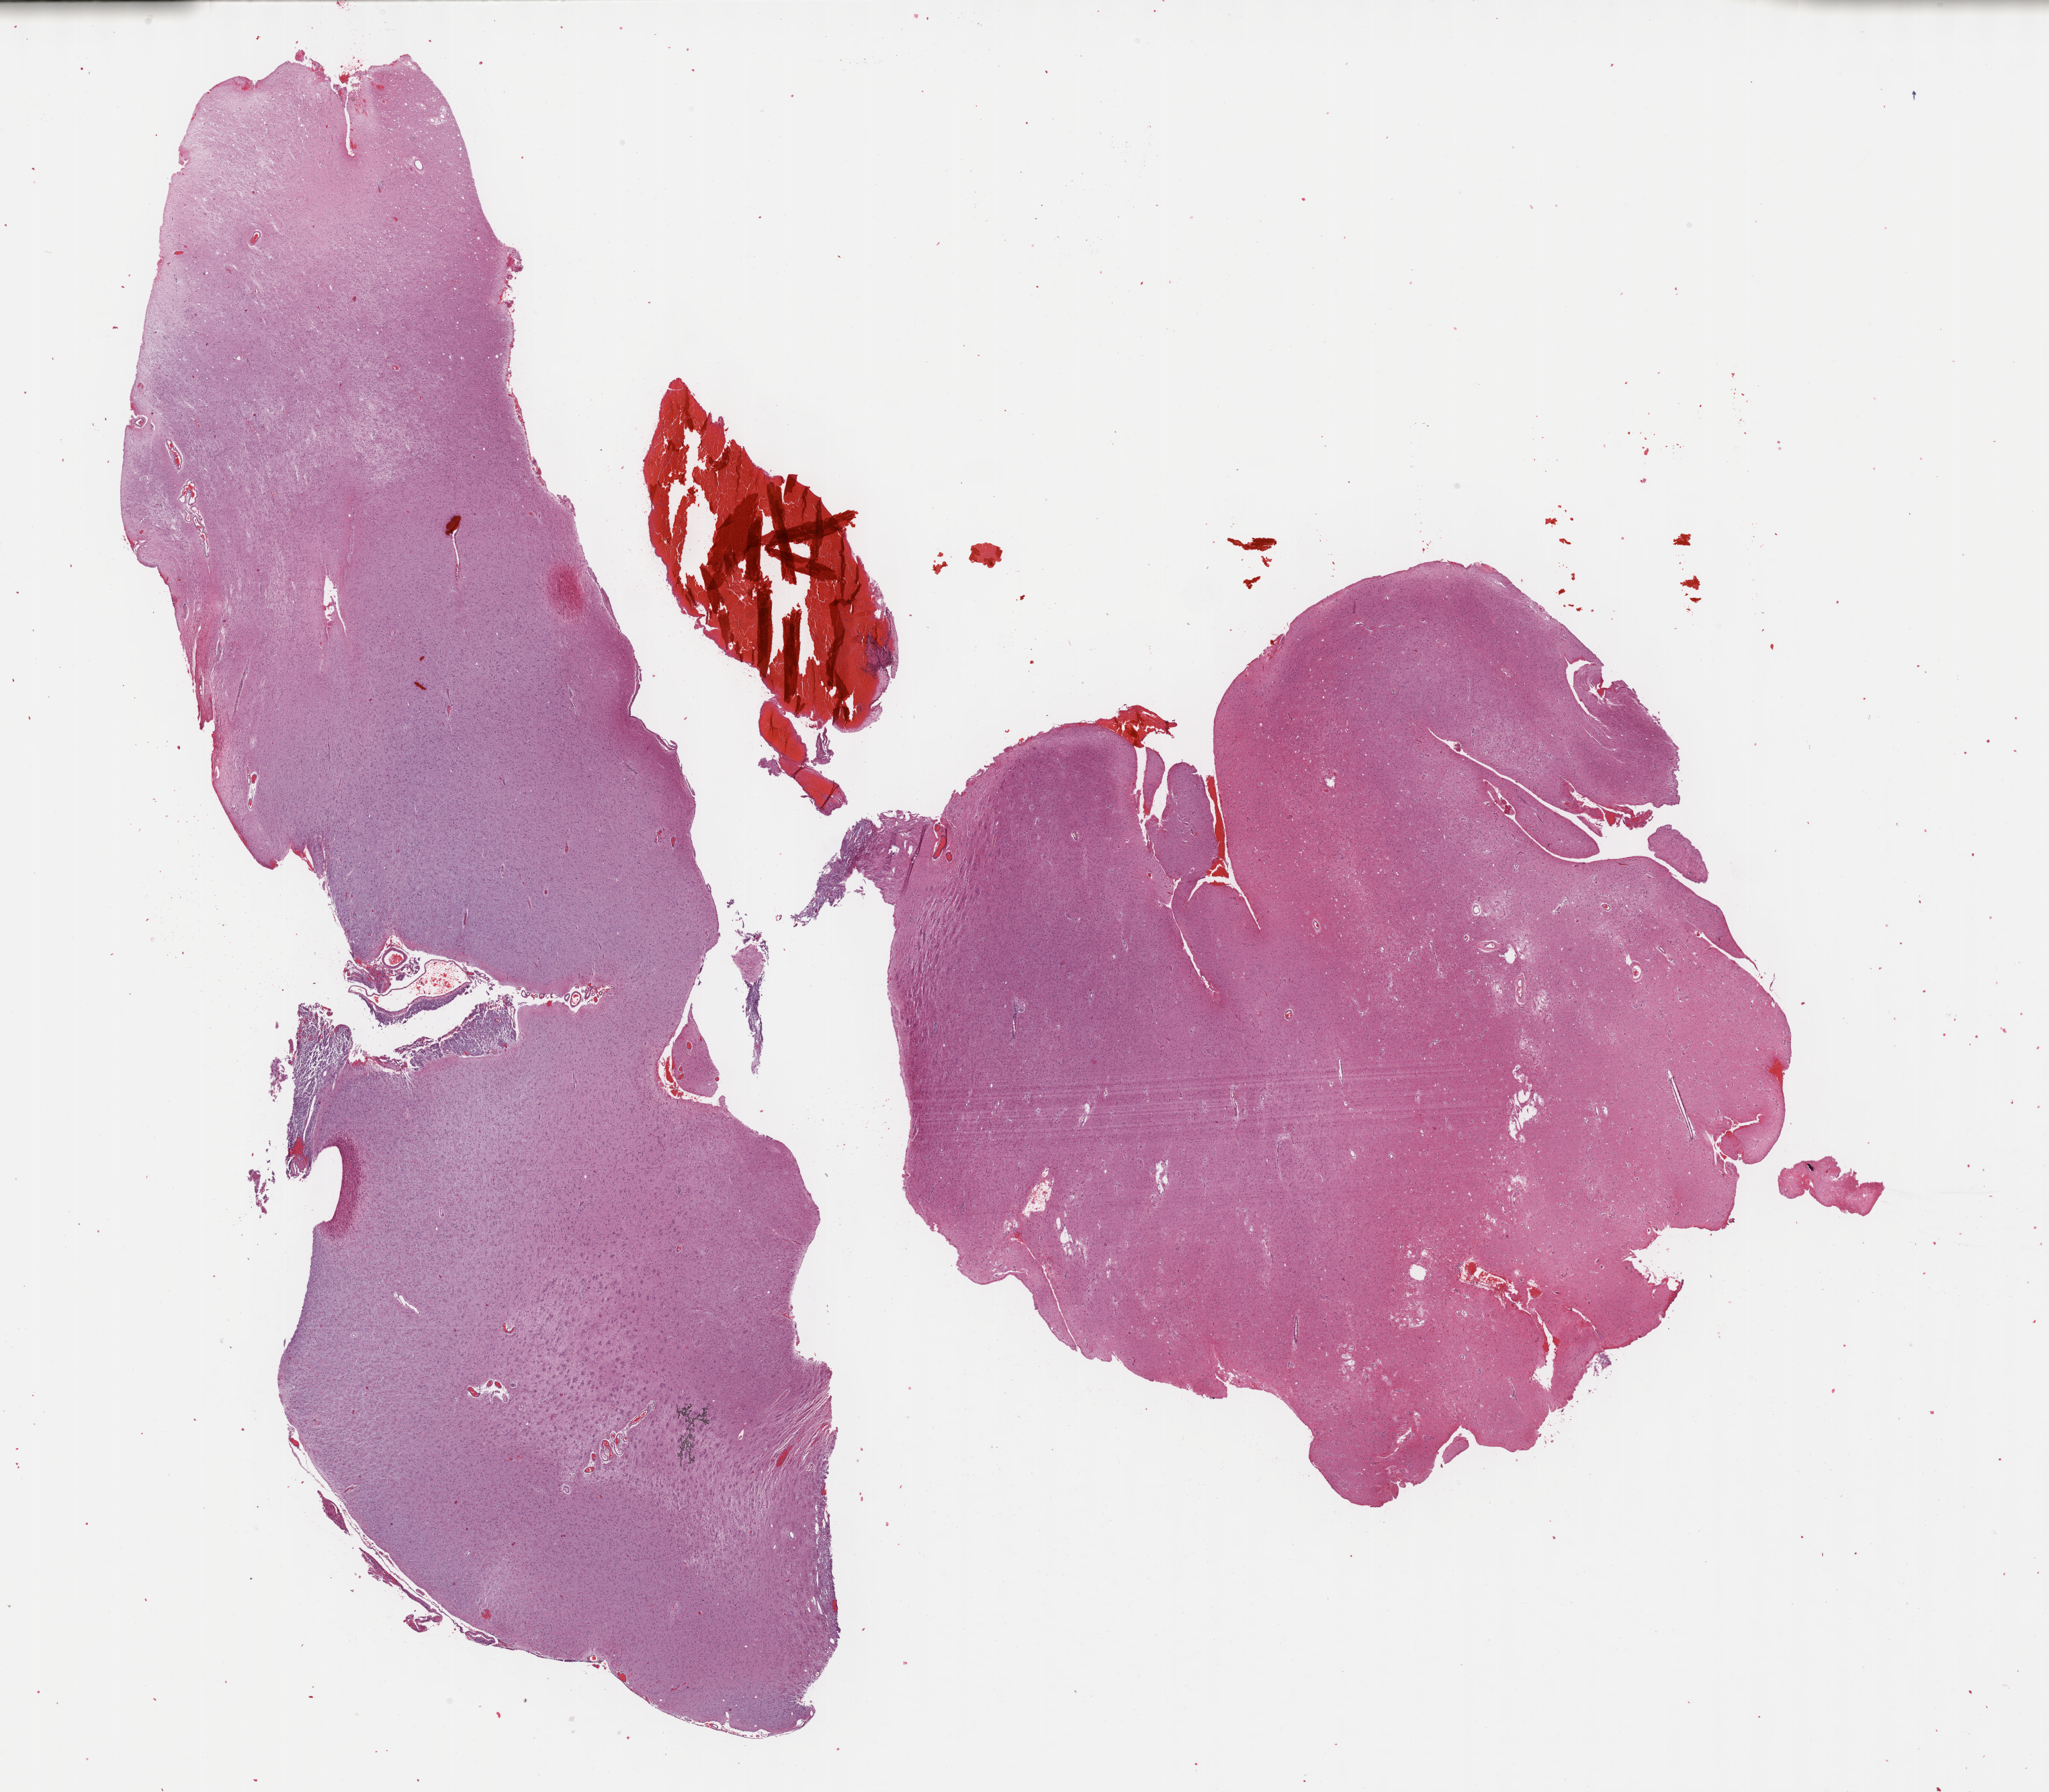
Digitized Hematoxylin and eosin (H&E) stained tissue section (whole slide), low-resolution overview of the scanned area, about 24.7 x 21.6 mm, formalin-fixed paraffin-embedded (FFPE) diagnostic section, brain, primary tumour sample. Patient: male, age at initial diagnosis 58 years. Histologic grade: G3 (poorly differentiated).
Laterality: left. Diagnosis: Mixed glioma.